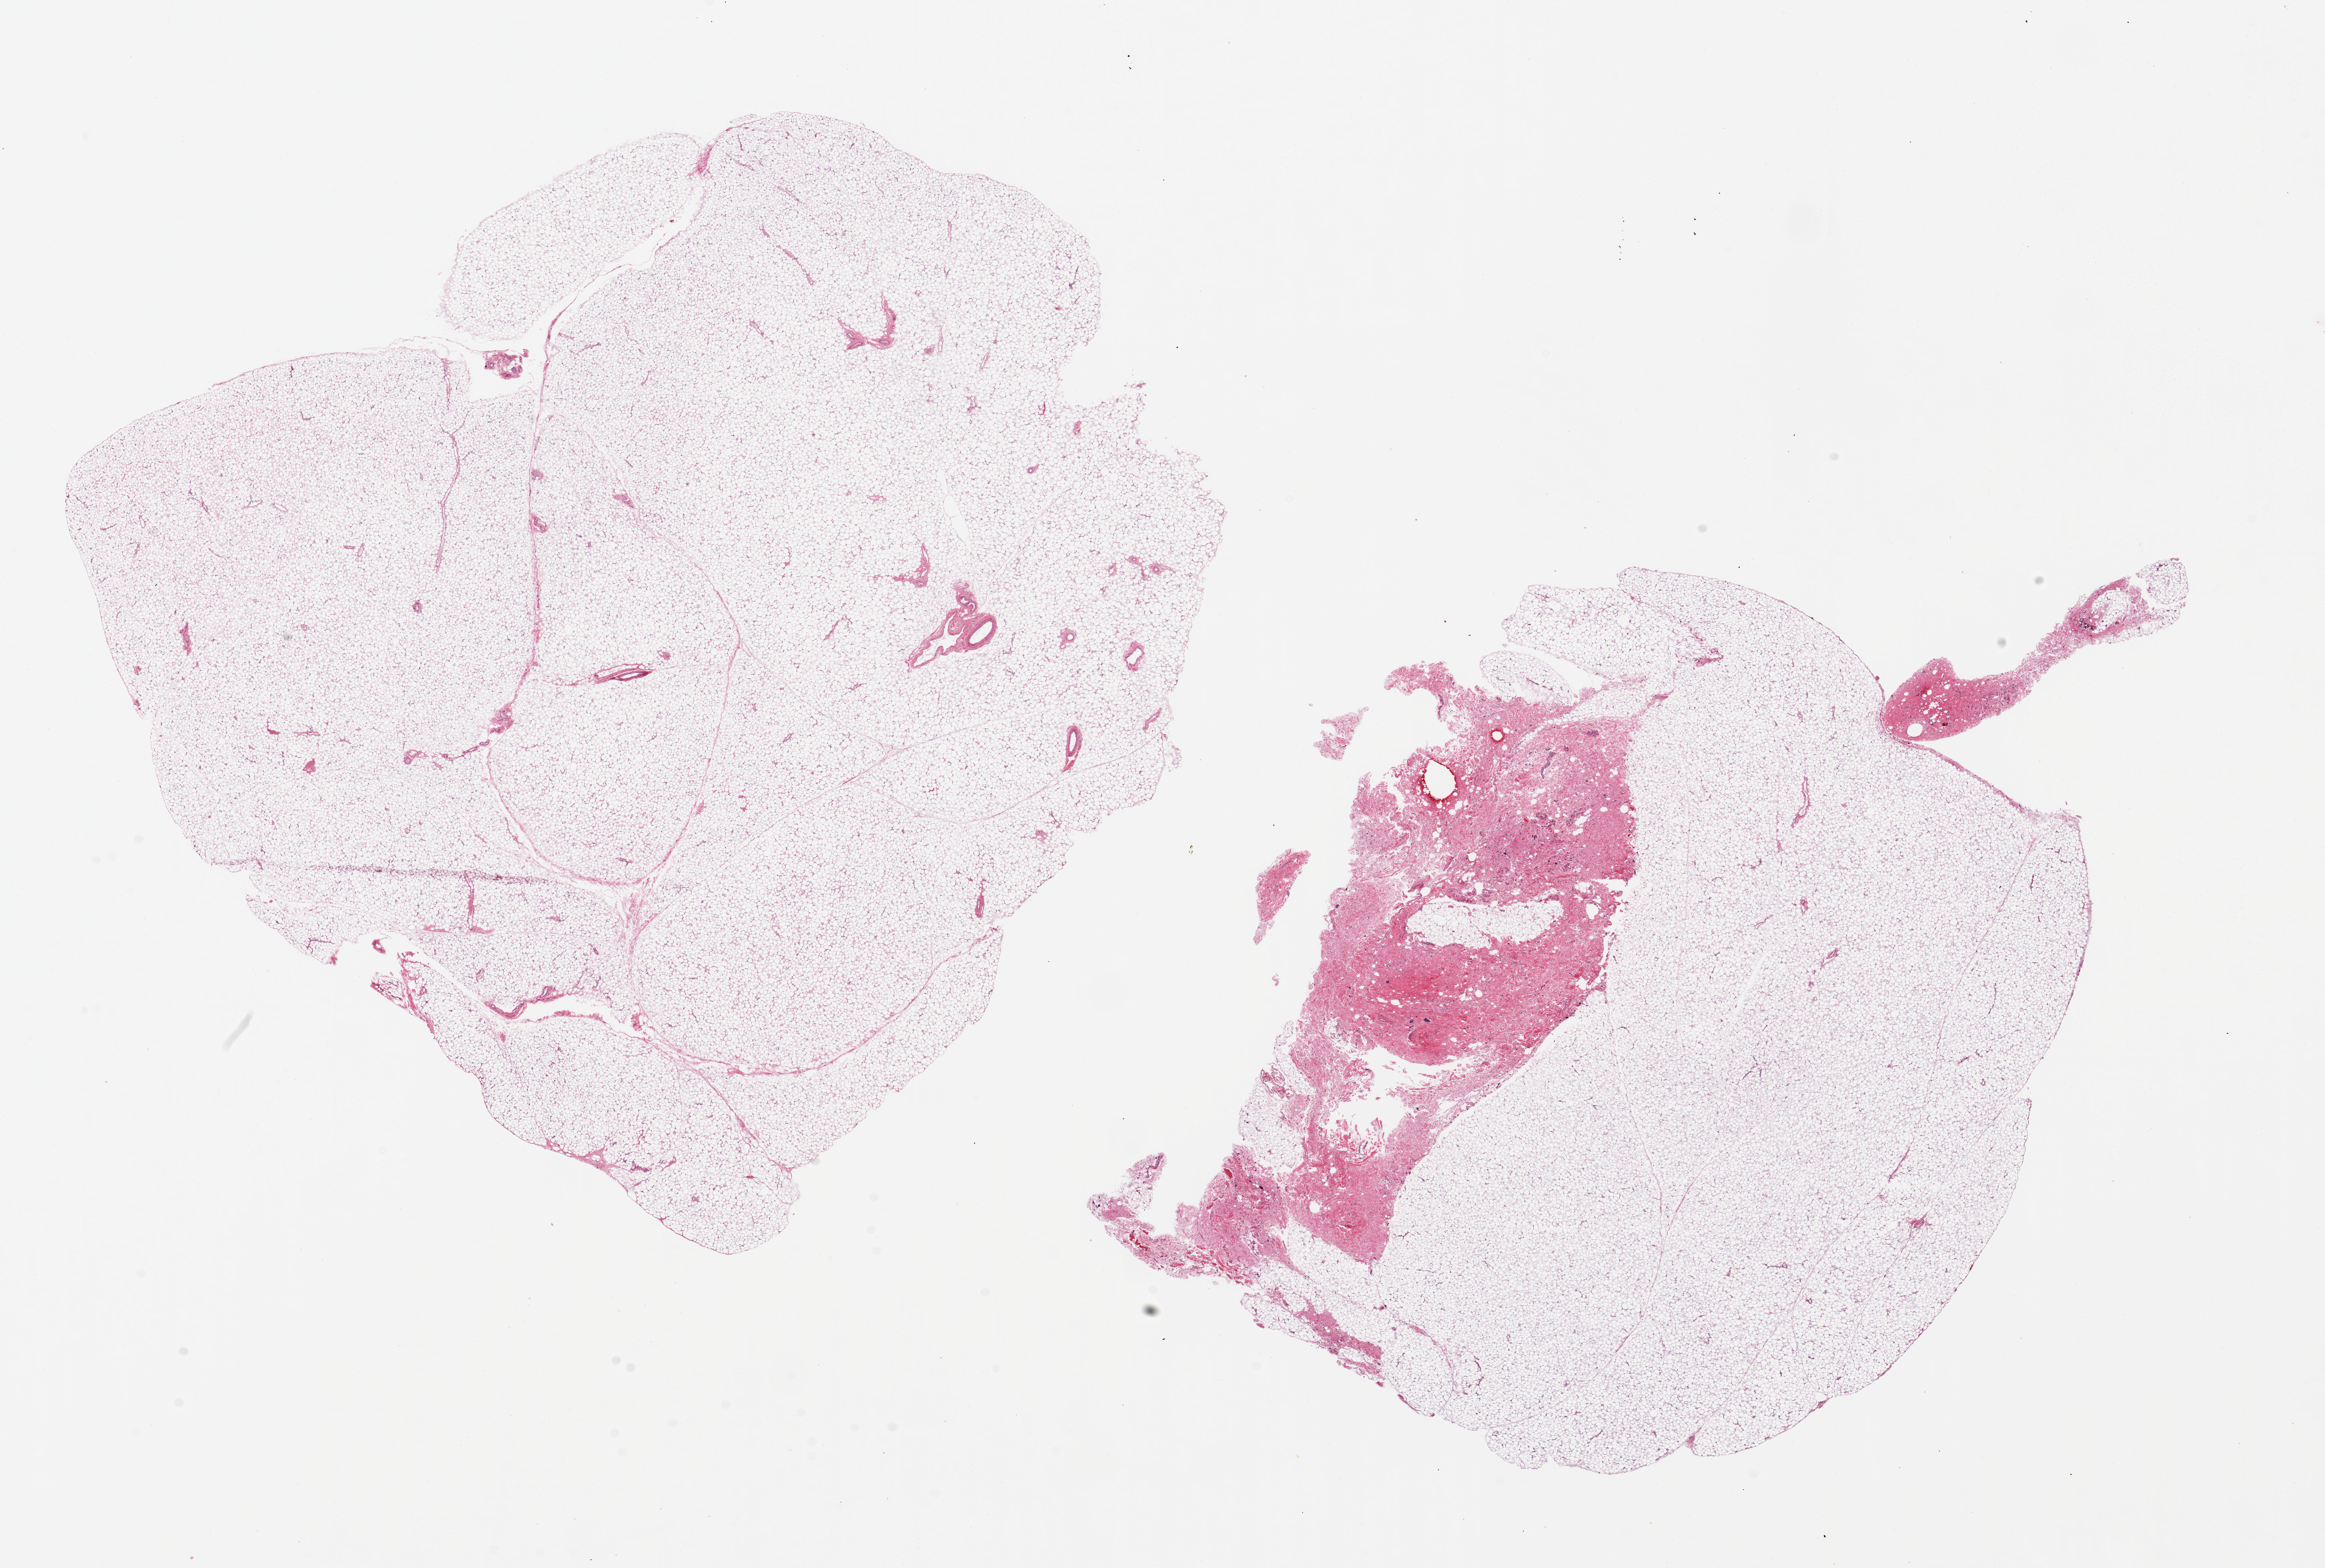
Digitized haematoxylin and eosin-stained section, brightfield, a low-resolution overview of the entire scanned area, about 27.6 x 18.6 mm (acquisition: 20x scan). PAXgene-fixed paraffin-embedded (PFPE) section. Section of adrenal gland (target tissue). Tissue donor sample. Donor sex: female.
Reviewer comment on this tissue sample: 2 pieces, 13x10 & 13x12mm; All adipose tissue, no adrenal tissue.